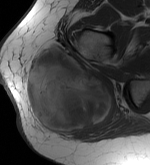
MRI of an extremity soft-tissue mass, one axial slice; MR volume resampled by the dataset authors to the PET/CT grid (not the native acquisition matrix); 3.27 mm slice thickness; 150 × 165 image matrix, field of view 146 × 161 mm. Female patient. From the clinical record (not read from this slice): histological type: epithelioid sarcoma with vascular differentiation; site of the primary tumour: right buttock.
Outlined on this slice (expert contour drawn on MRI and transferred to this co-registered scan by the dataset authors):
- gross tumour volume (mass): bounding box [x1, y1, x2, y2] px = [25, 45, 115, 137]